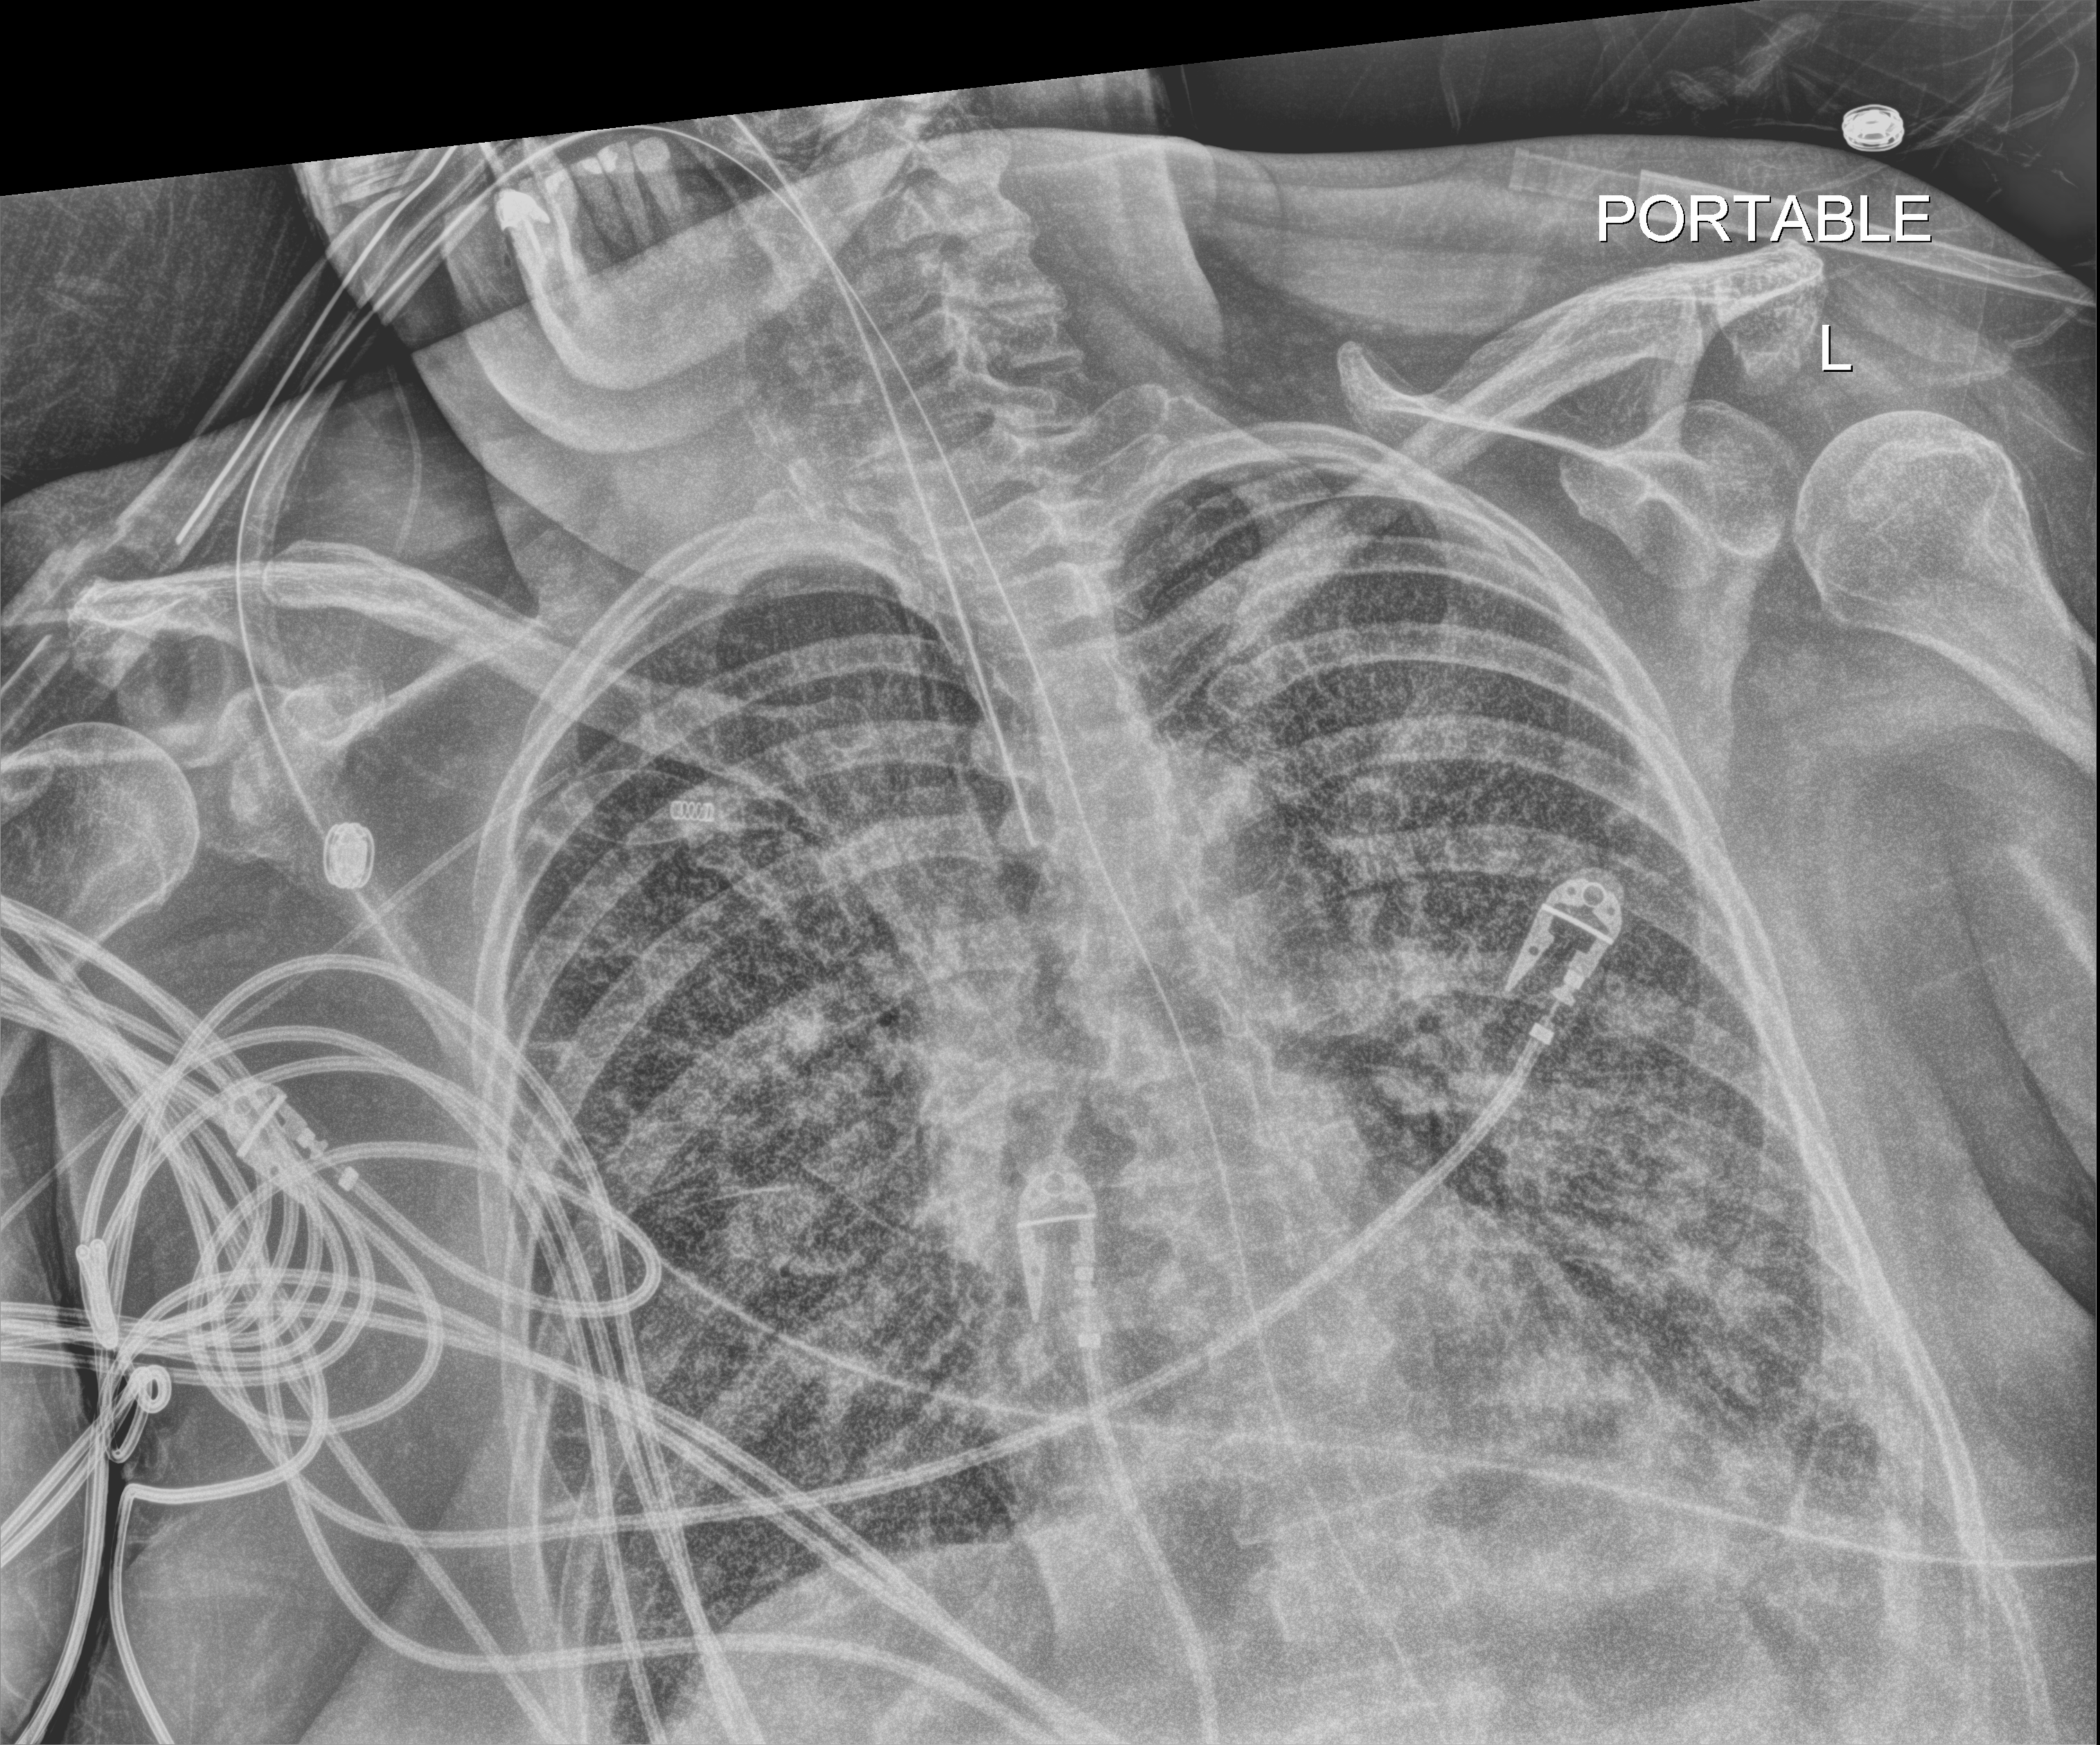
Bedside chest radiograph (digital radiography). Female patient hospitalised with COVID-19, age 60–74 years.
From the hospital-stay record, not from the radiograph (when in the stay this image was taken is not recorded):
- mechanically ventilated during this hospital stay: yes
- other chronic lung disease (admission record): no